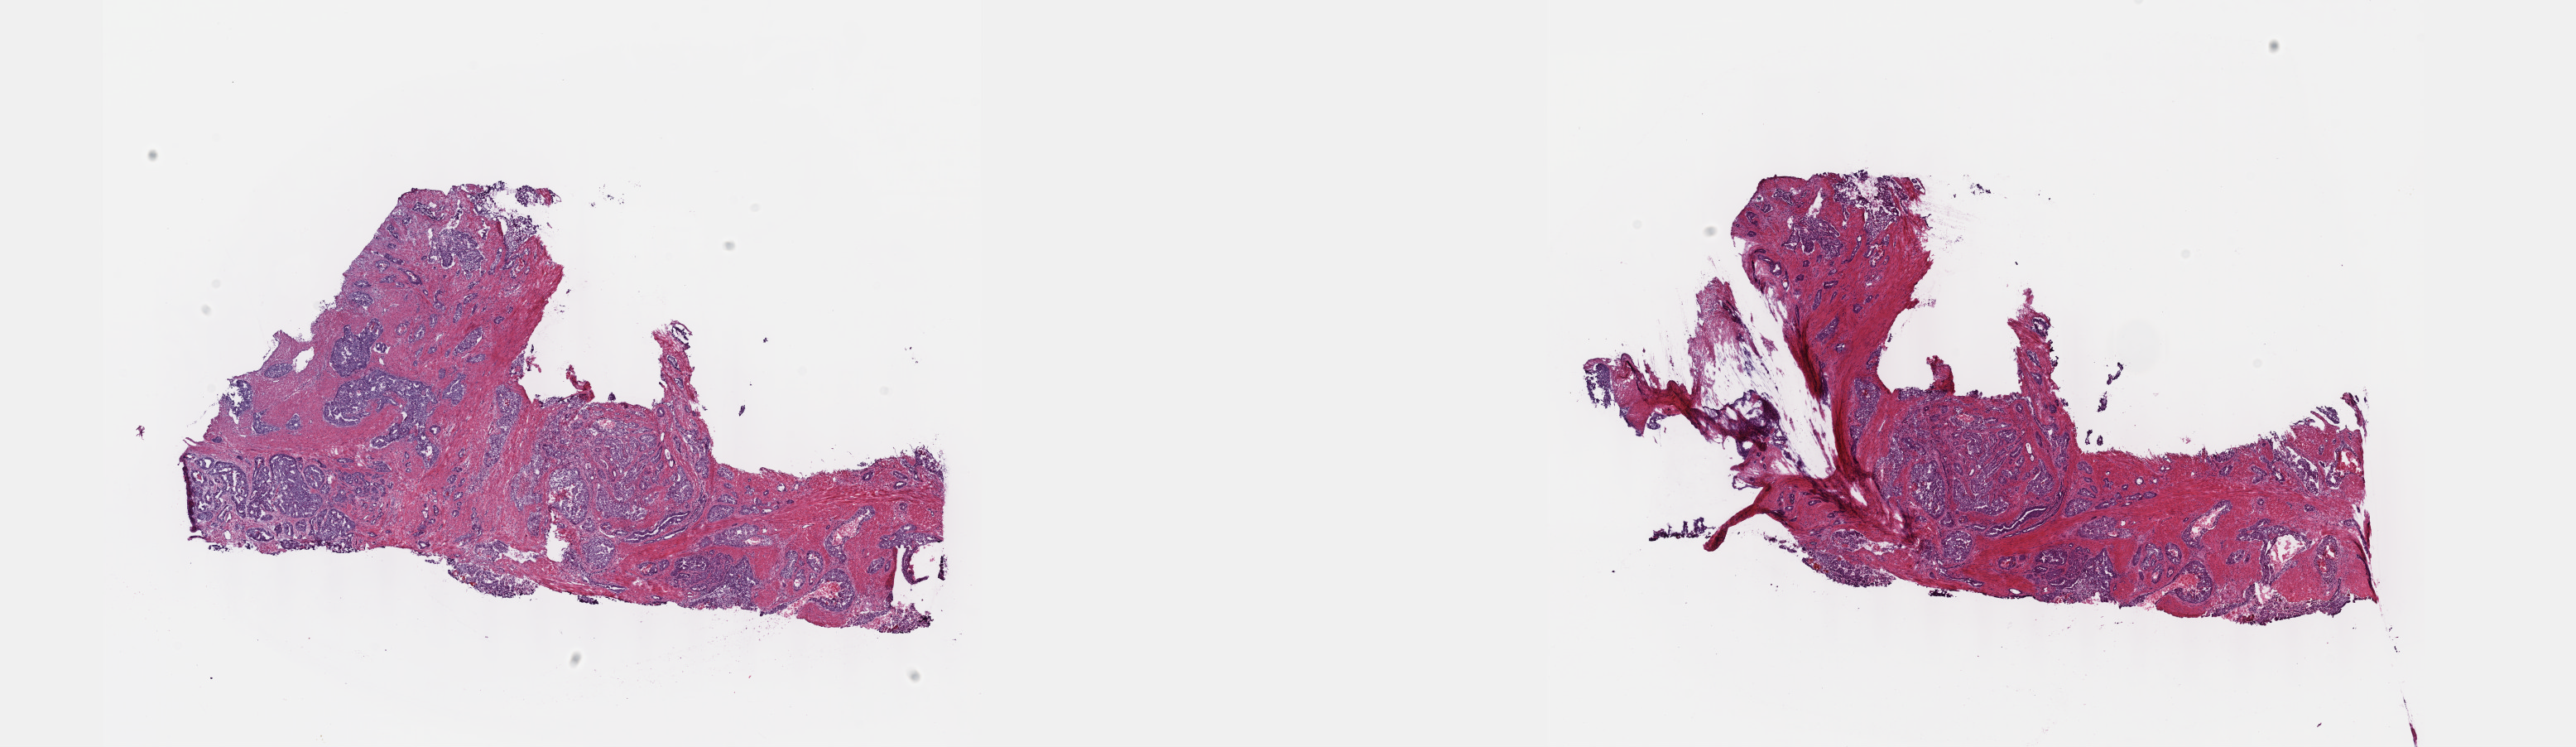
Digitized Hematoxylin and eosin (H&E) stained tissue section (whole slide) — low-resolution overview of the scanned area, about 25.1 x 7.3 mm, frozen section from the top of the tissue portion, primary tumour sample from the prostate. Male patient; age at initial diagnosis 67 years. Gleason score: 9 (4+5). Pathologist review of this section (percent, as recorded): tumour cells 60%, tumour nuclei 60%, normal cells 0%, stromal cells 40%, necrosis 0%. Infiltration values recorded for this section: lymphocyte infiltration 40%, monocyte infiltration 20%, neutrophil infiltration 20%.
Lymph nodes positive (case pathology): 1 of 2 examined. Histologic diagnosis: Adenocarcinoma, NOS. Laterality: bilateral.